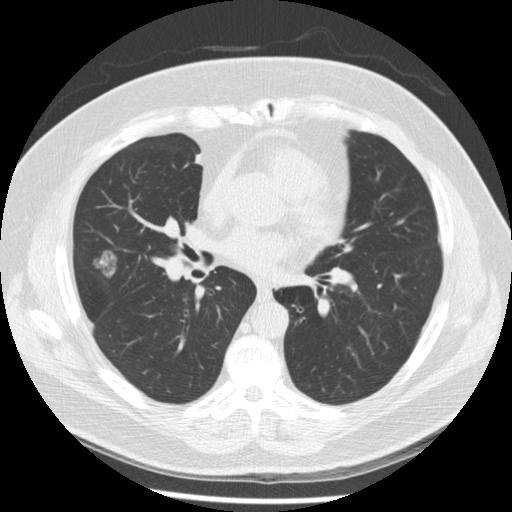
Low-dose screening chest CT, one axial slice. Position 114 of 230 along the scan axis. Reconstruction kernel STANDARD. 120 kVp. Lung window (W 1500 / L -600 HU). 2.5 mm slice thickness. 512 × 512 image matrix, field of view 360 × 360 mm.
Outlined on this slice (expert manual segmentation):
- lesion 1 (tumor, middle lobe of right lung): box from (x=95, y=252) to (x=117, y=278) px